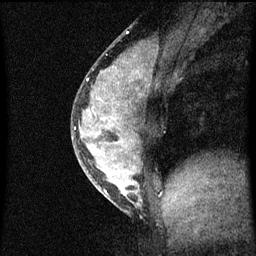
Breast MRI (dynamic contrast-enhanced), one sagittal slice. Position 29 of 60 along the scan axis. Dynamic contrast-enhanced series, image 2 of 3 at this slice position (ordered by acquisition). 1.5 T. TE 4.2 ms, TR 8 ms. 2 mm slice thickness. 256 × 256 image matrix, field of view 180 × 180 mm. Patient: female, 33 years.
Annotated regions visible in this slice (semi-automatic segmentation, software-assisted and operator-edited):
- analysis volume of interest (the breast-tissue region the enhancement analysis was run in; not a lesion): bounding box [x1, y1, x2, y2] px = [71, 56, 157, 215]
- tumour enhancement mask (voxels above the 70 % enhancement threshold inside the analysis volume of interest): [75, 70, 147, 205]